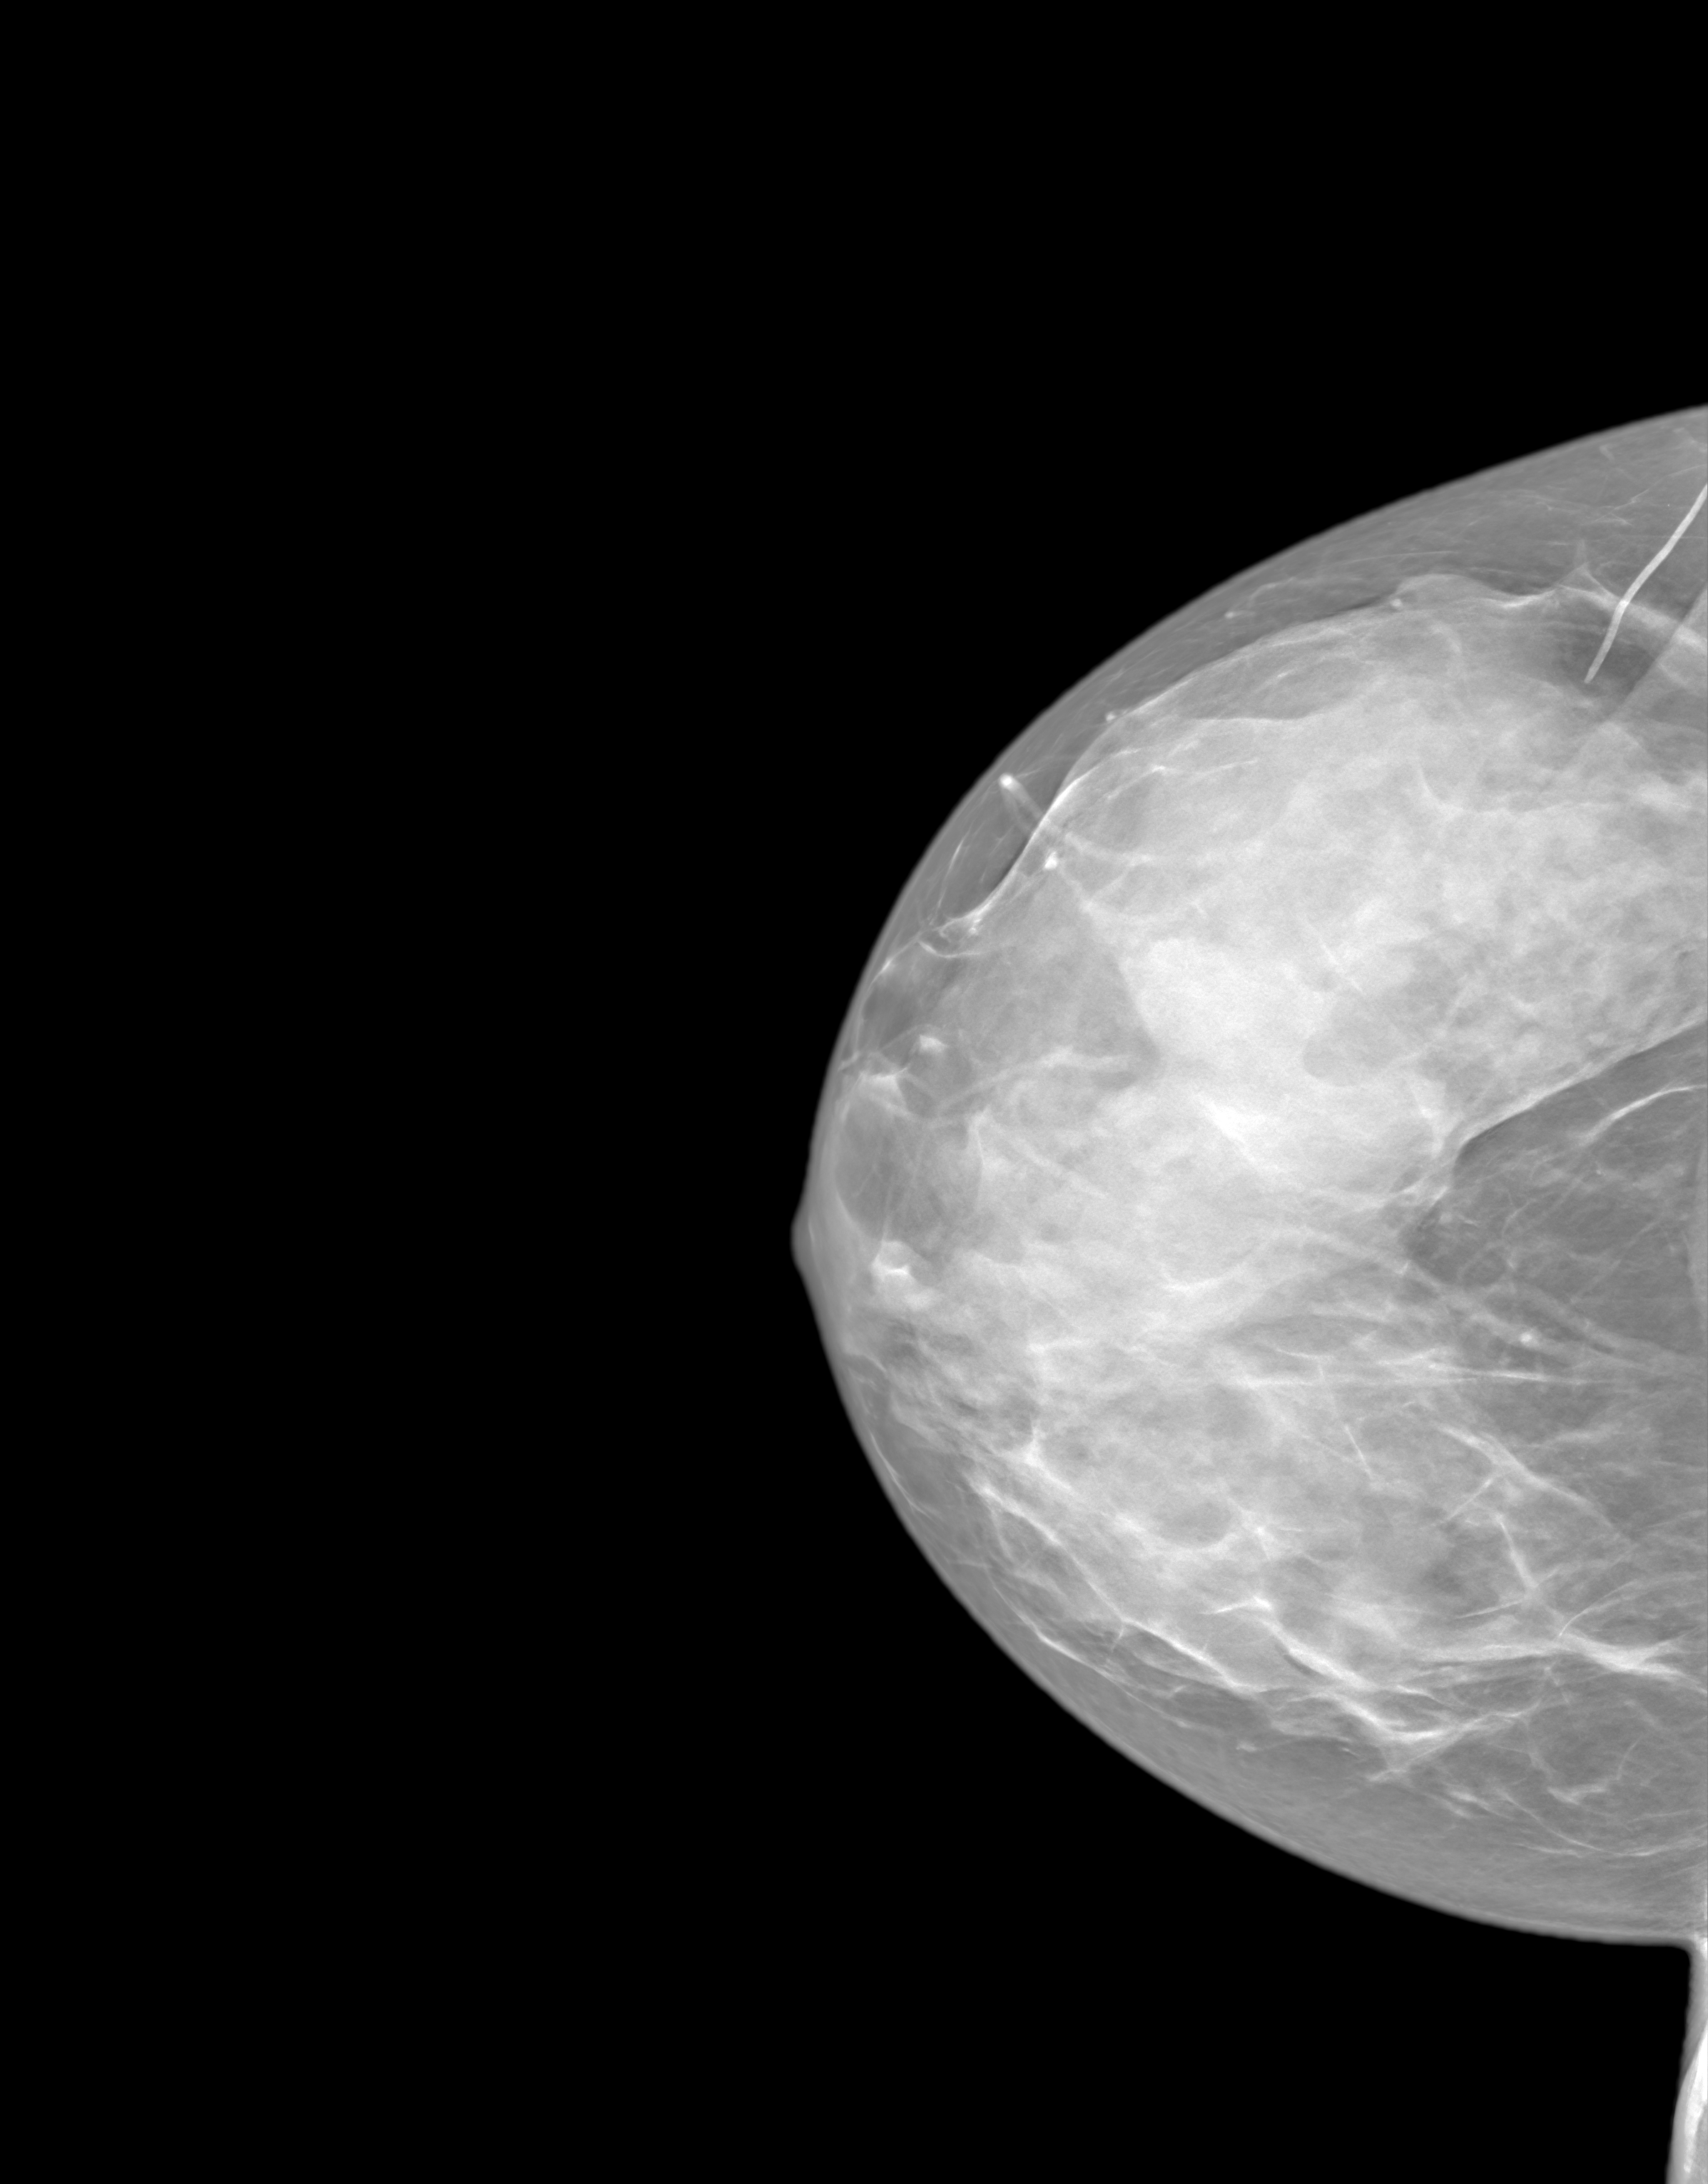
Screening examination. Female patient, age 43 years.
Image type: synthesized 2-D view from tomosynthesis. Breast: right. Projection: craniocaudal (CC) view. Breast density at the screening exam (both breasts): extremely dense (BI-RADS density category d). Final BI-RADS assessment for this screening round (tomosynthesis exam, both breasts): category 1. Recall: no recall after this screen.